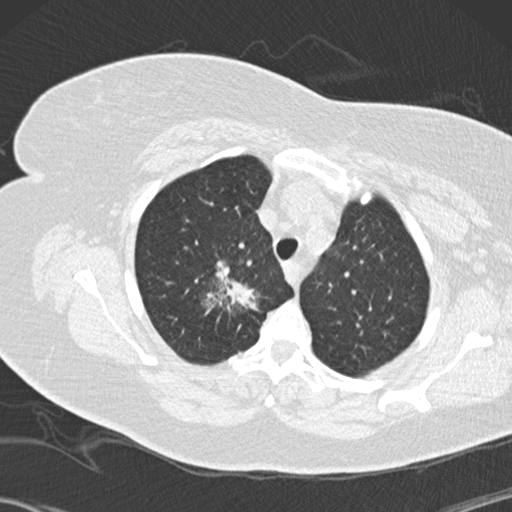
Low-dose screening chest CT, one axial slice. Slice 116 of 146 in the series (ordered by position). 120 kVp. Lung window (W 1500 / L -600 HU). 2 mm slice thickness. 512 × 512 image matrix, field of view 350 × 350 mm.
Outlined on this slice (outlined manually by an expert reader):
- lesion 1 (tumor, upper lobe of right lung): bounding box (x1, y1, x2, y2) in pixels: (206, 261, 258, 313)